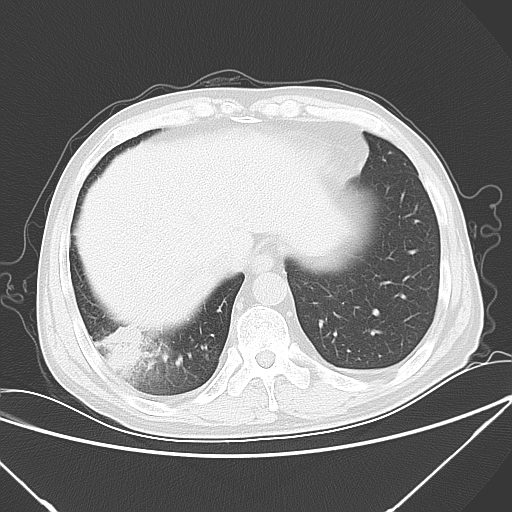
Chest CT, one axial slice. Slice 16 of 57 in the series (ordered by position). 120 kVp. Lung window (W 1500 / L -600 HU). 5 mm slice thickness. 512 × 512 image matrix, field of view 364 × 364 mm. Patient: male, 54 years. Case-level facts recorded for this patient, not image findings: clinical TNM (as recorded): T2 N1 M0.
Structures marked on this image (bounding box drawn by a radiologist):
- lung tumour (recorded histology: adenocarcinoma): box from (x=92, y=321) to (x=147, y=377) px